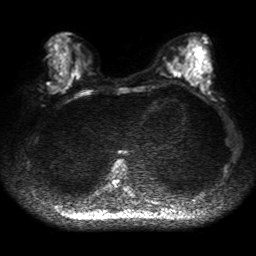
Breast MRI, one axial slice. Position 18 of 50 along the scan axis. Diffusion-weighted series; image 2 of 4 stored at this slice position (different b-values; order by instance number). 1.5 T. 4 mm slice thickness. 256 × 256 image matrix. Female patient.
Annotated regions visible in this slice (manually delineated by an expert):
- tumour on diffusion-weighted imaging: box from (x=47, y=82) to (x=60, y=94) px